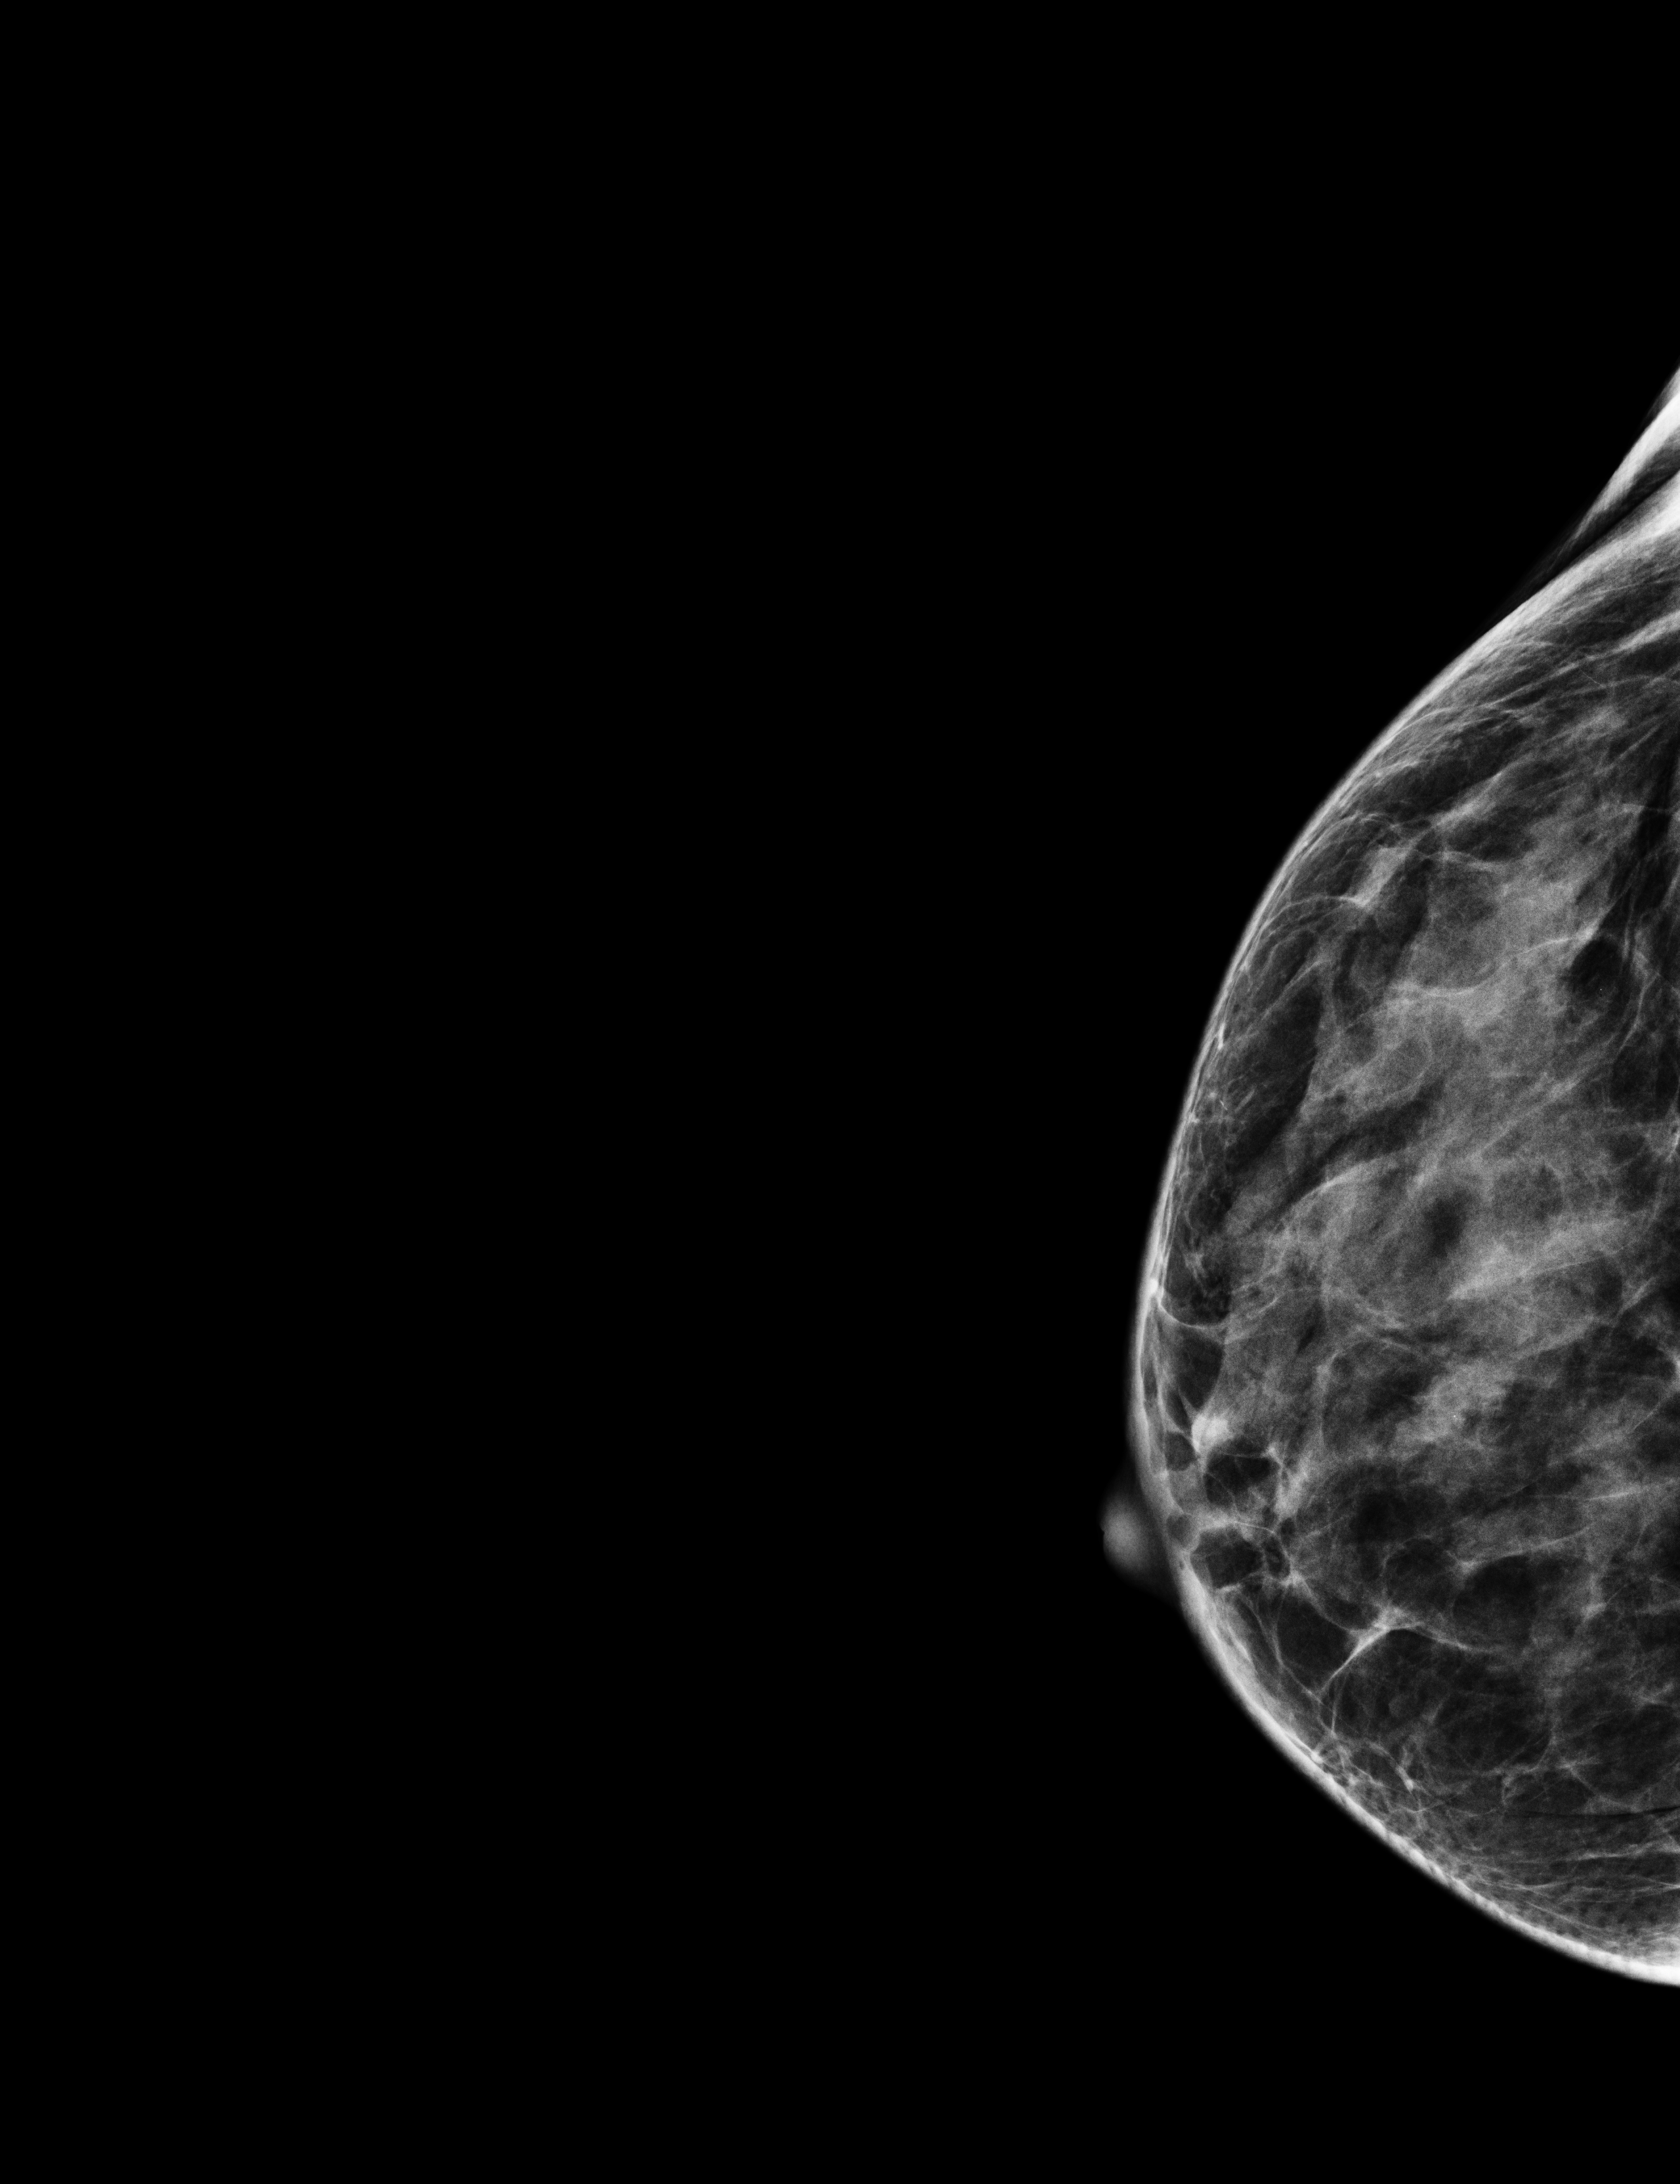
Digital mammogram (FFDM); right breast; exaggerated CC view (lateral); screening examination; compressed breast thickness 32 mm. Patient aged 52 years (female).
BI-RADS breast density category at the screening exam (both breasts, scale 1–4): 3. Final BI-RADS assessment for this screening round (tomosynthesis exam, both breasts): category 1. Recall: no recall after this screen.